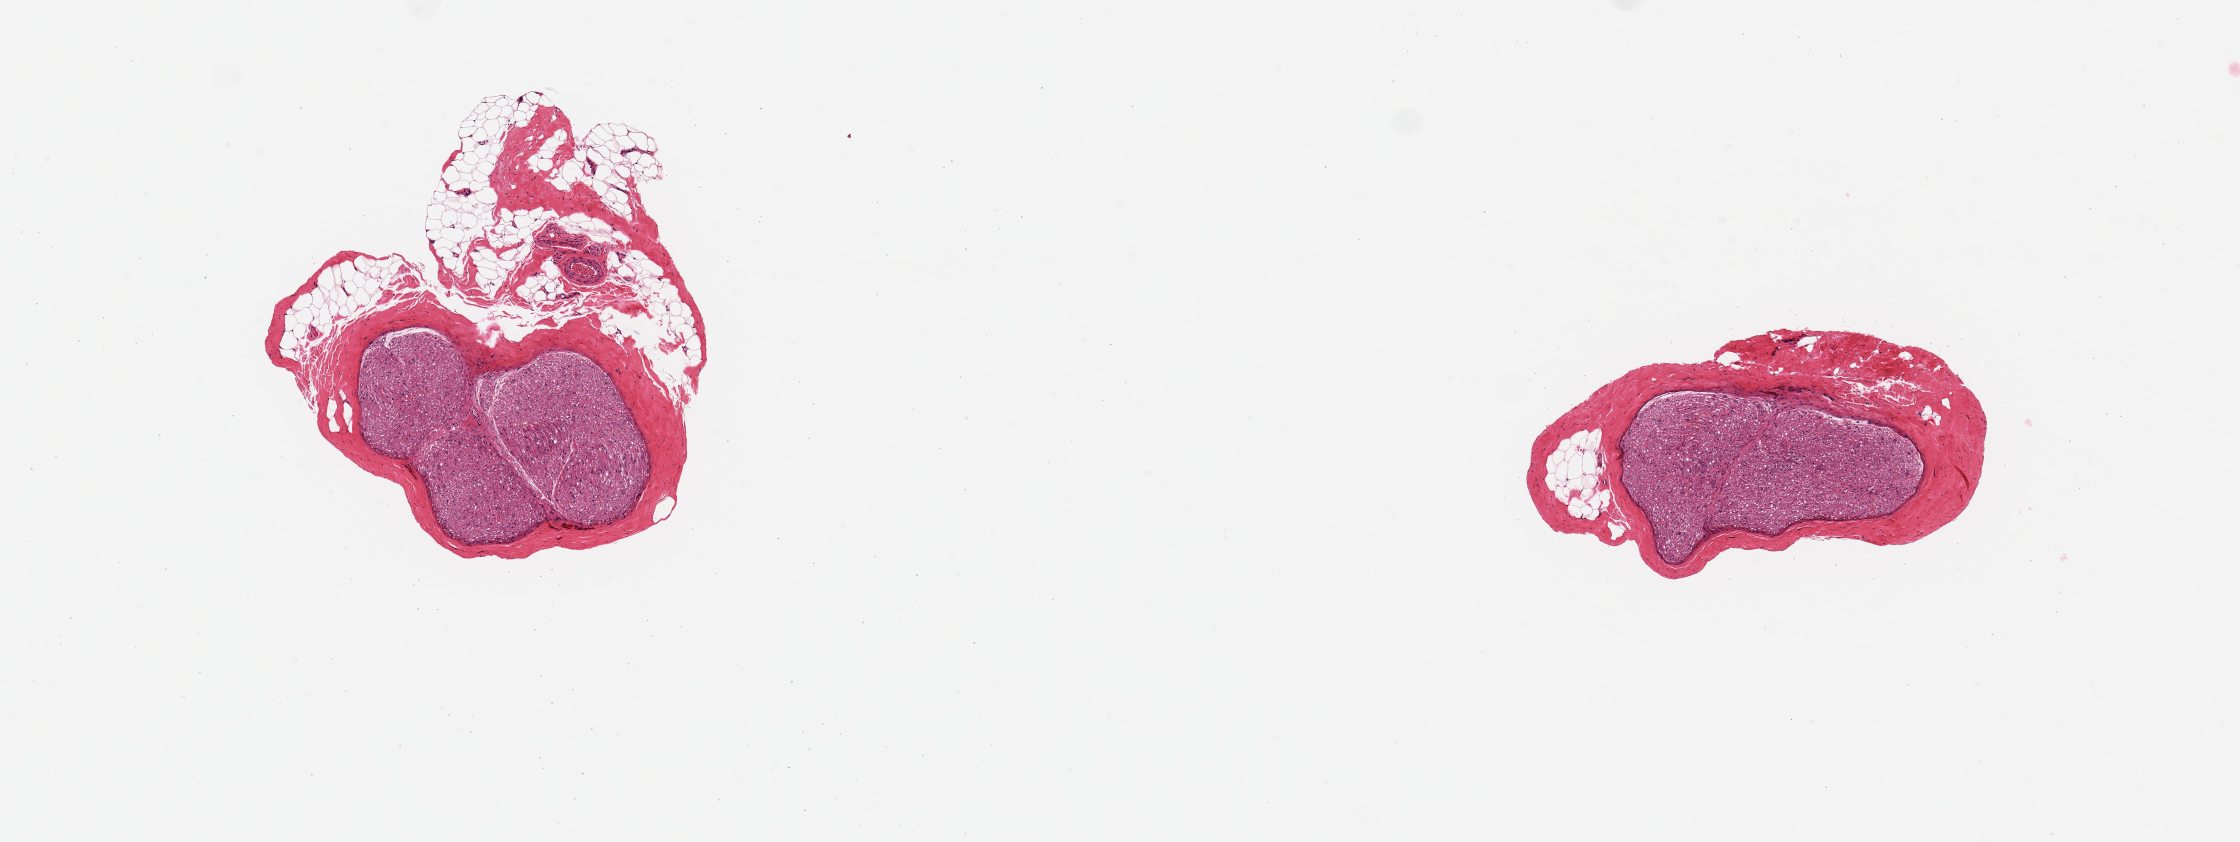
H&E whole-slide image — low-resolution overview of the scanned area, about 8.9 x 3.3 mm. PAXgene-fixed, paraffin-embedded tissue. Section of tibial nerve (target tissue). Tissue donor sample. Female donor.
Reviewer comment on this tissue sample: 2 pieces, up to 1.8x1.3 mm; 1 with 50% fat; 1 with 10% fat.